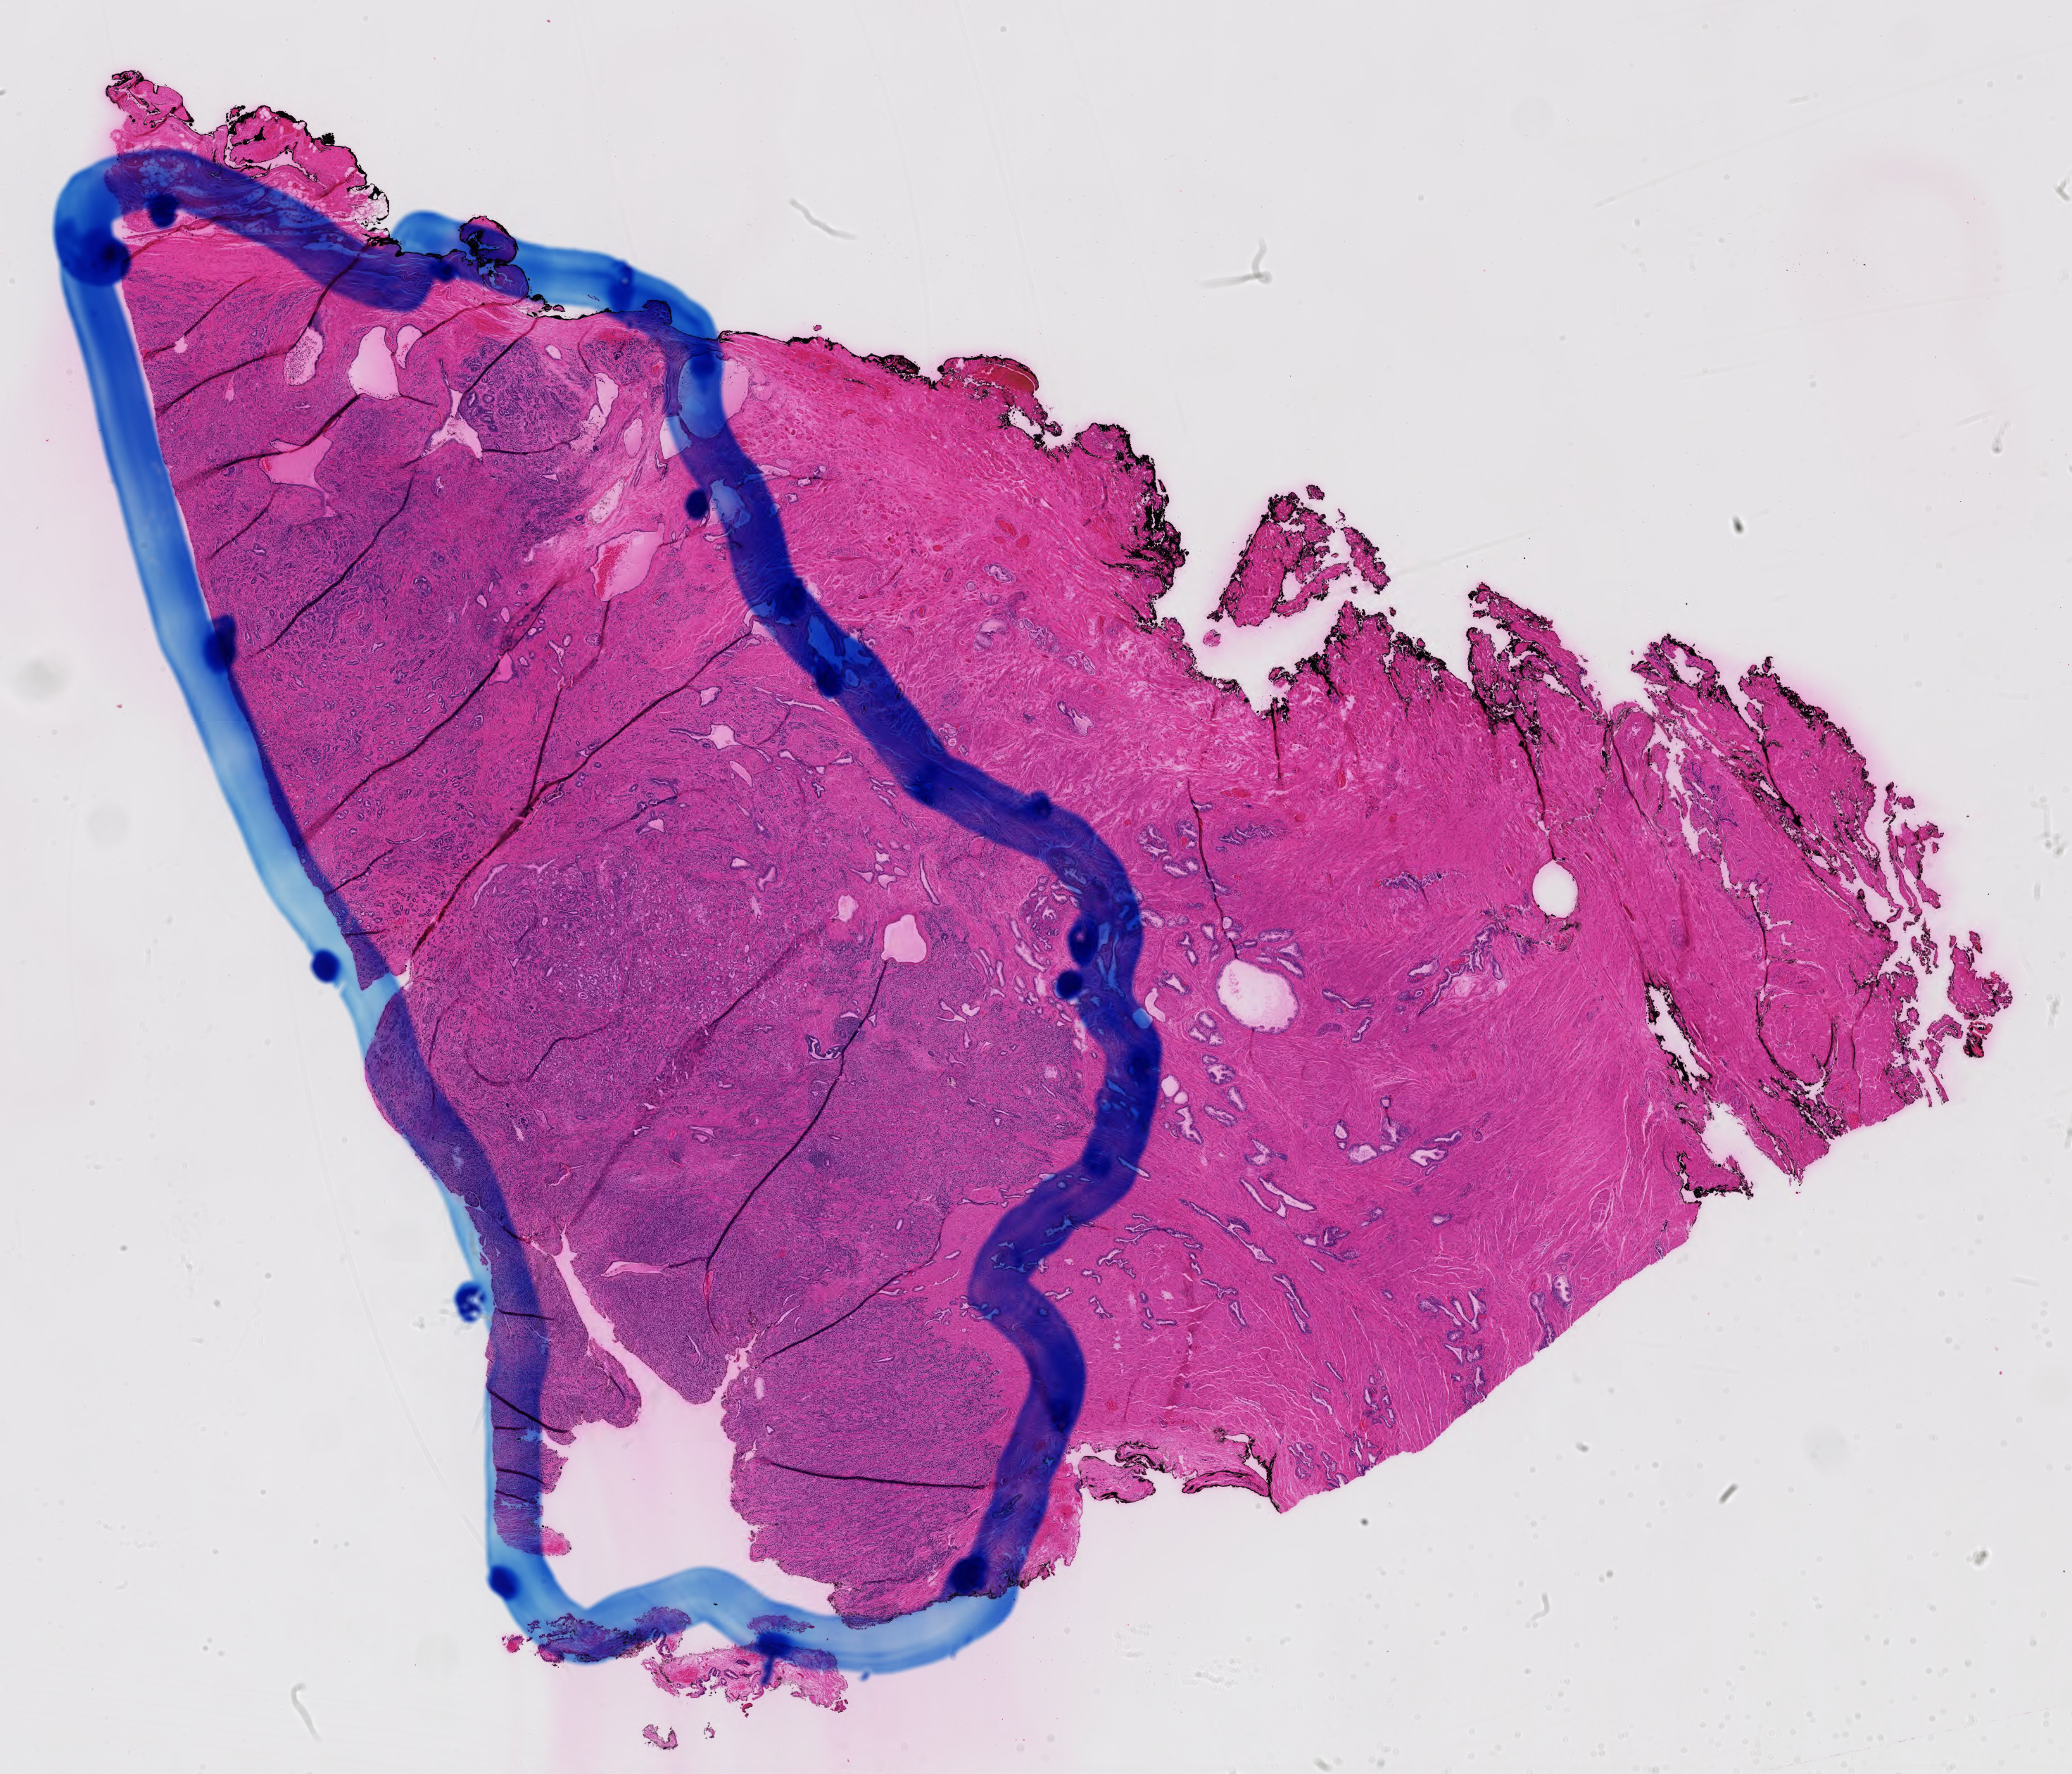
Digitized H&E-stained tissue section (whole slide), low-resolution overview of the scanned area, about 21.4 x 18.3 mm (acquisition: 40x scan). FFPE section. Primary tumour sample from the prostate. Patient: male, age at initial diagnosis 67 years. Gleason score: 9 (4+5).
* lymph nodes positive (case pathology): 4 of 20 examined
* histologic diagnosis: Adenocarcinoma, NOS (prostate gland)